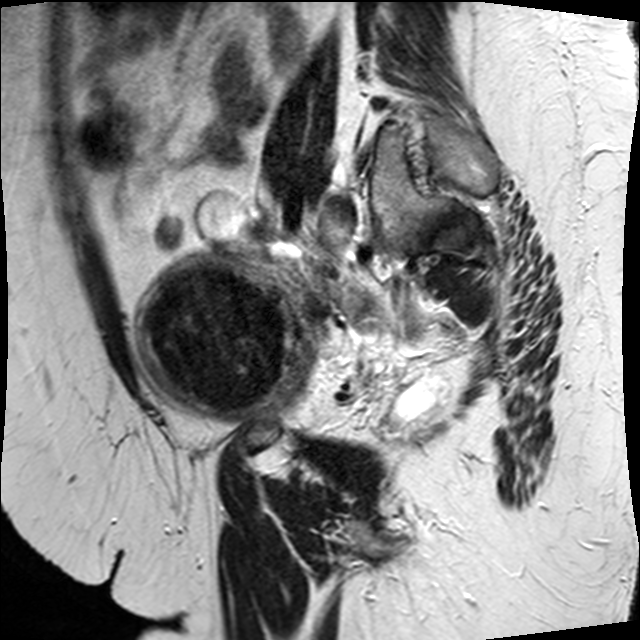
Pelvic MRI for cervical cancer, one sagittal slice. Position 9 of 34 along the scan axis. T2-weighted. 1.5 T. TE 89 ms, TR 3320 ms. 4 mm slice thickness. 640 × 640 image matrix, field of view 260 × 260 mm. Patient: female, 50 years.
Structures marked on this image (manually delineated by an expert):
- uterus and cervix: bounding box [x1, y1, x2, y2] px = [131, 239, 325, 424]